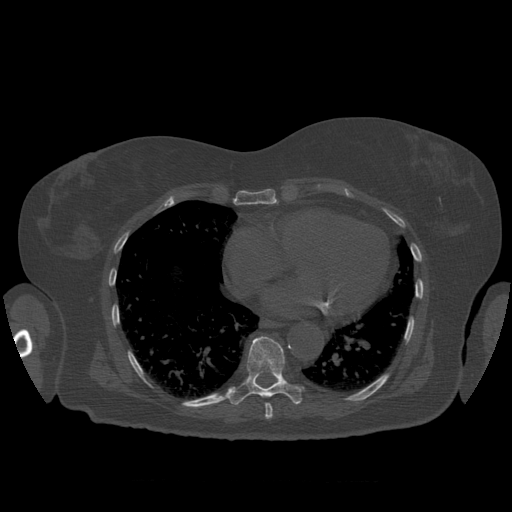
CT including the spine, one axial slice. Position 362 of 399 along the scan axis. Bone window (W 1800 / L 400 HU). 1.25 mm slice thickness. 512 × 512 image matrix. Patient age 81 years. Case-level facts recorded for this patient, not image findings: primary cancer: renal.
Structures marked on this image (semi-automatically segmented with operator editing):
- T8 vertebra: box from (x=265, y=403) to (x=273, y=420) px
- T9 vertebra: (x=229, y=336)–(x=303, y=405)